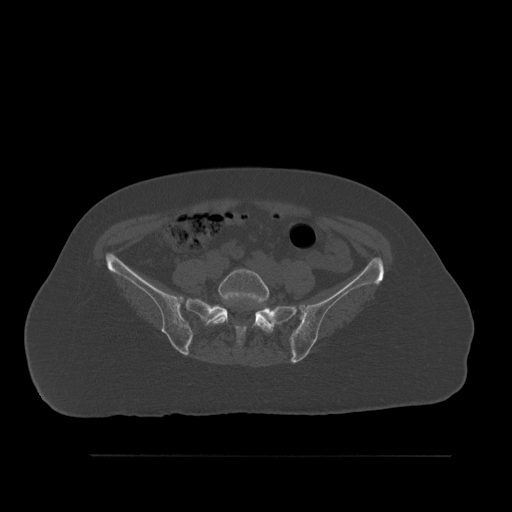
CT including the spine, one axial slice; position 181 of 527 along the scan axis; bone window (W 1800 / L 400 HU); 512 × 512 image matrix, field of view 470 × 470 mm. Patient: female, 73 years. Case-level facts recorded for this patient, not image findings: primary cancer: breast; vertebrae with lytic lesions (as recorded): L2.
Structures marked on this image (semi-automatic segmentation, software-assisted and operator-edited):
- L5 vertebra: bounding box <209,268,273,333> (left, top, right, bottom; pixels)